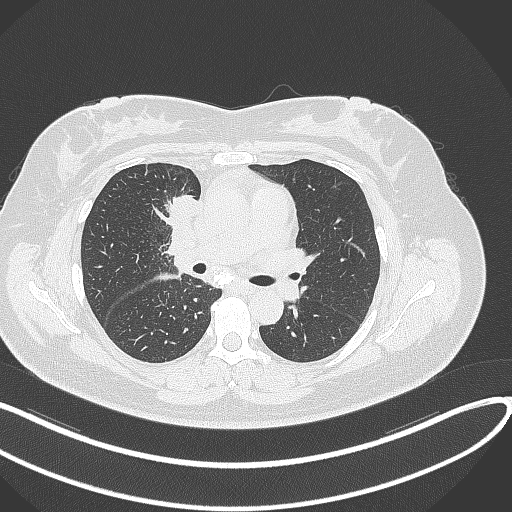
Chest CT, one axial slice; position 159 of 303 along the scan axis; lung window (W 1500 / L -600 HU); 512 × 512 image matrix, field of view 400 × 400 mm. Female patient, age 46 years. From the clinical record (not read from this slice): clinical TNM (as recorded): T2a N1 M0.
Structures marked on this image (rectangle marked by the reading radiologist):
- lung tumour (recorded histology: adenocarcinoma): bounding box <166,191,200,223> (left, top, right, bottom; pixels)